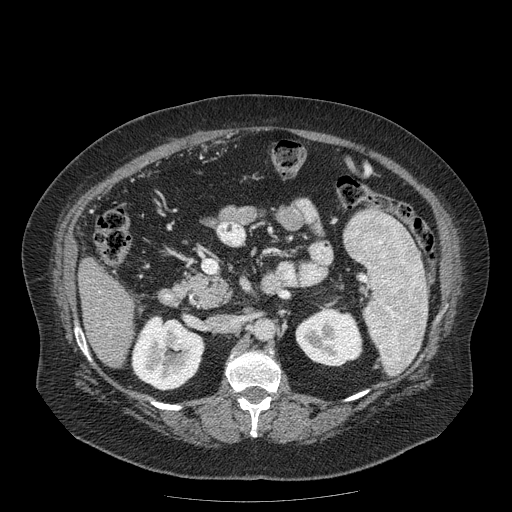
Contrast-enhanced abdominal CT (liver protocol), one axial slice. Position 67 of 204 along the scan axis. Reconstruction kernel STANDARD. 120 kVp. Soft-tissue window (W 400 / L 40 HU). 2.5 mm slice thickness. 512 × 512 image matrix. Case-level facts recorded for this patient, not image findings: diagnosis: hepatocellular carcinoma (patient treated with transarterial chemoembolisation; whether this scan precedes or follows treatment is not stated here); TNM stage (as recorded): Stage-IIIB.
Structures marked on this image (semi-automatically segmented with operator editing):
- liver parenchyma outside the tumour (the mass and vessels are separate outlines, so this box may not span the whole liver): bounding box (x1, y1, x2, y2) in pixels: (78, 258, 134, 368)